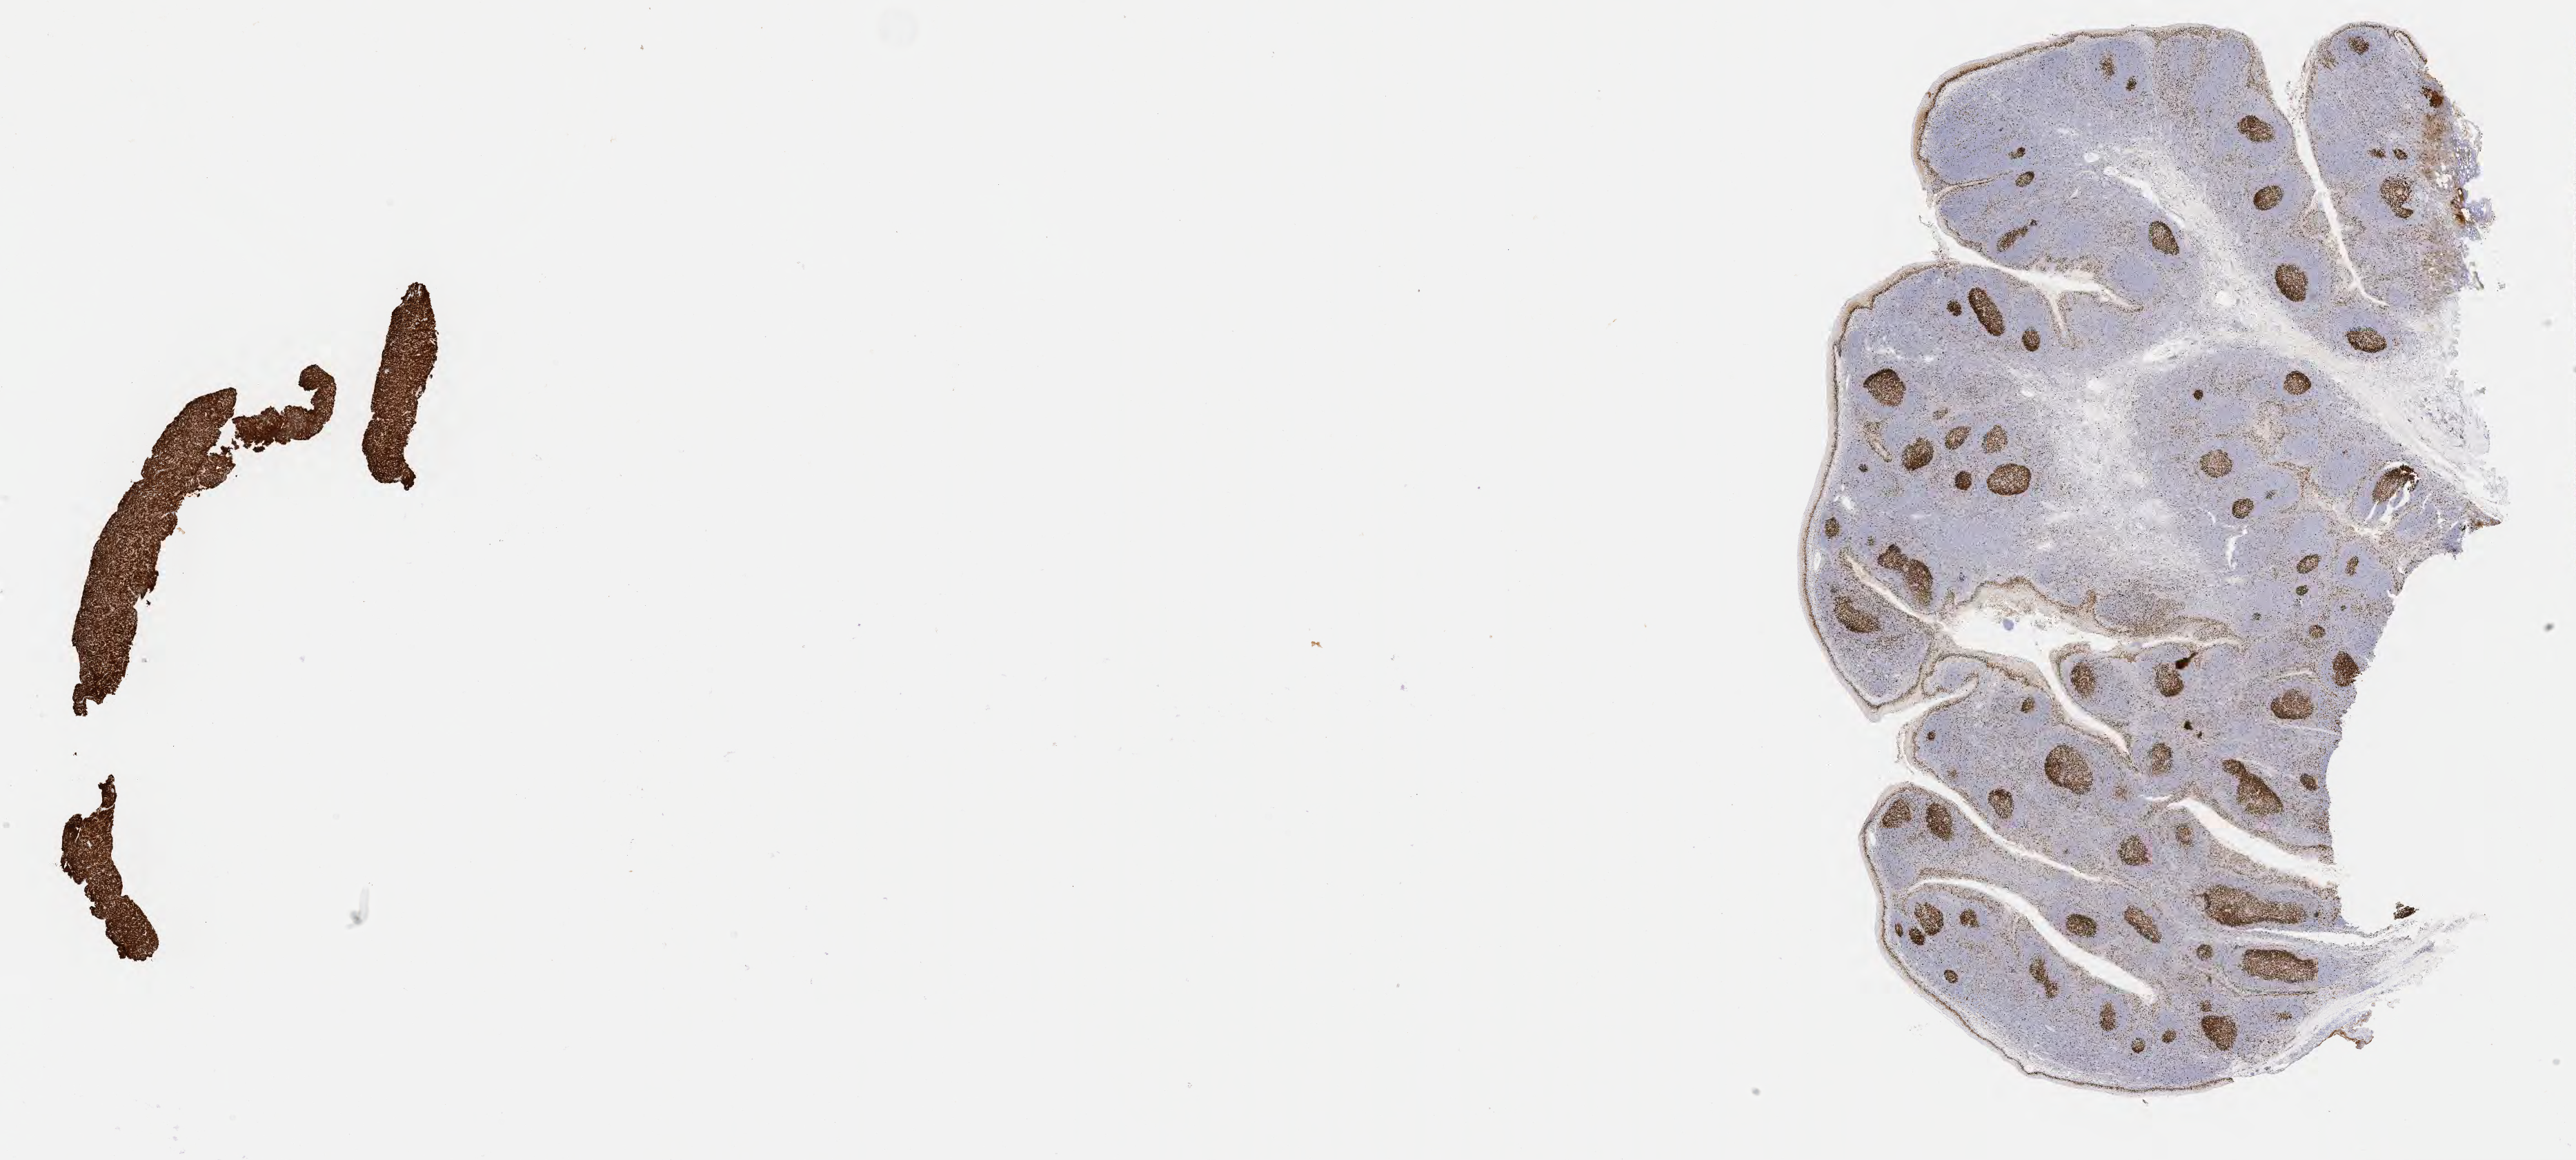
IHC for Ki-67, whole-slide image, shown as a low-resolution overview of the whole scanned area (about 30.2 x 13.6 mm), specimen: tumor tissue. Patient male; 10 years old.
Histologic diagnosis: Diffuse large B-cell lymphoma, NOS.